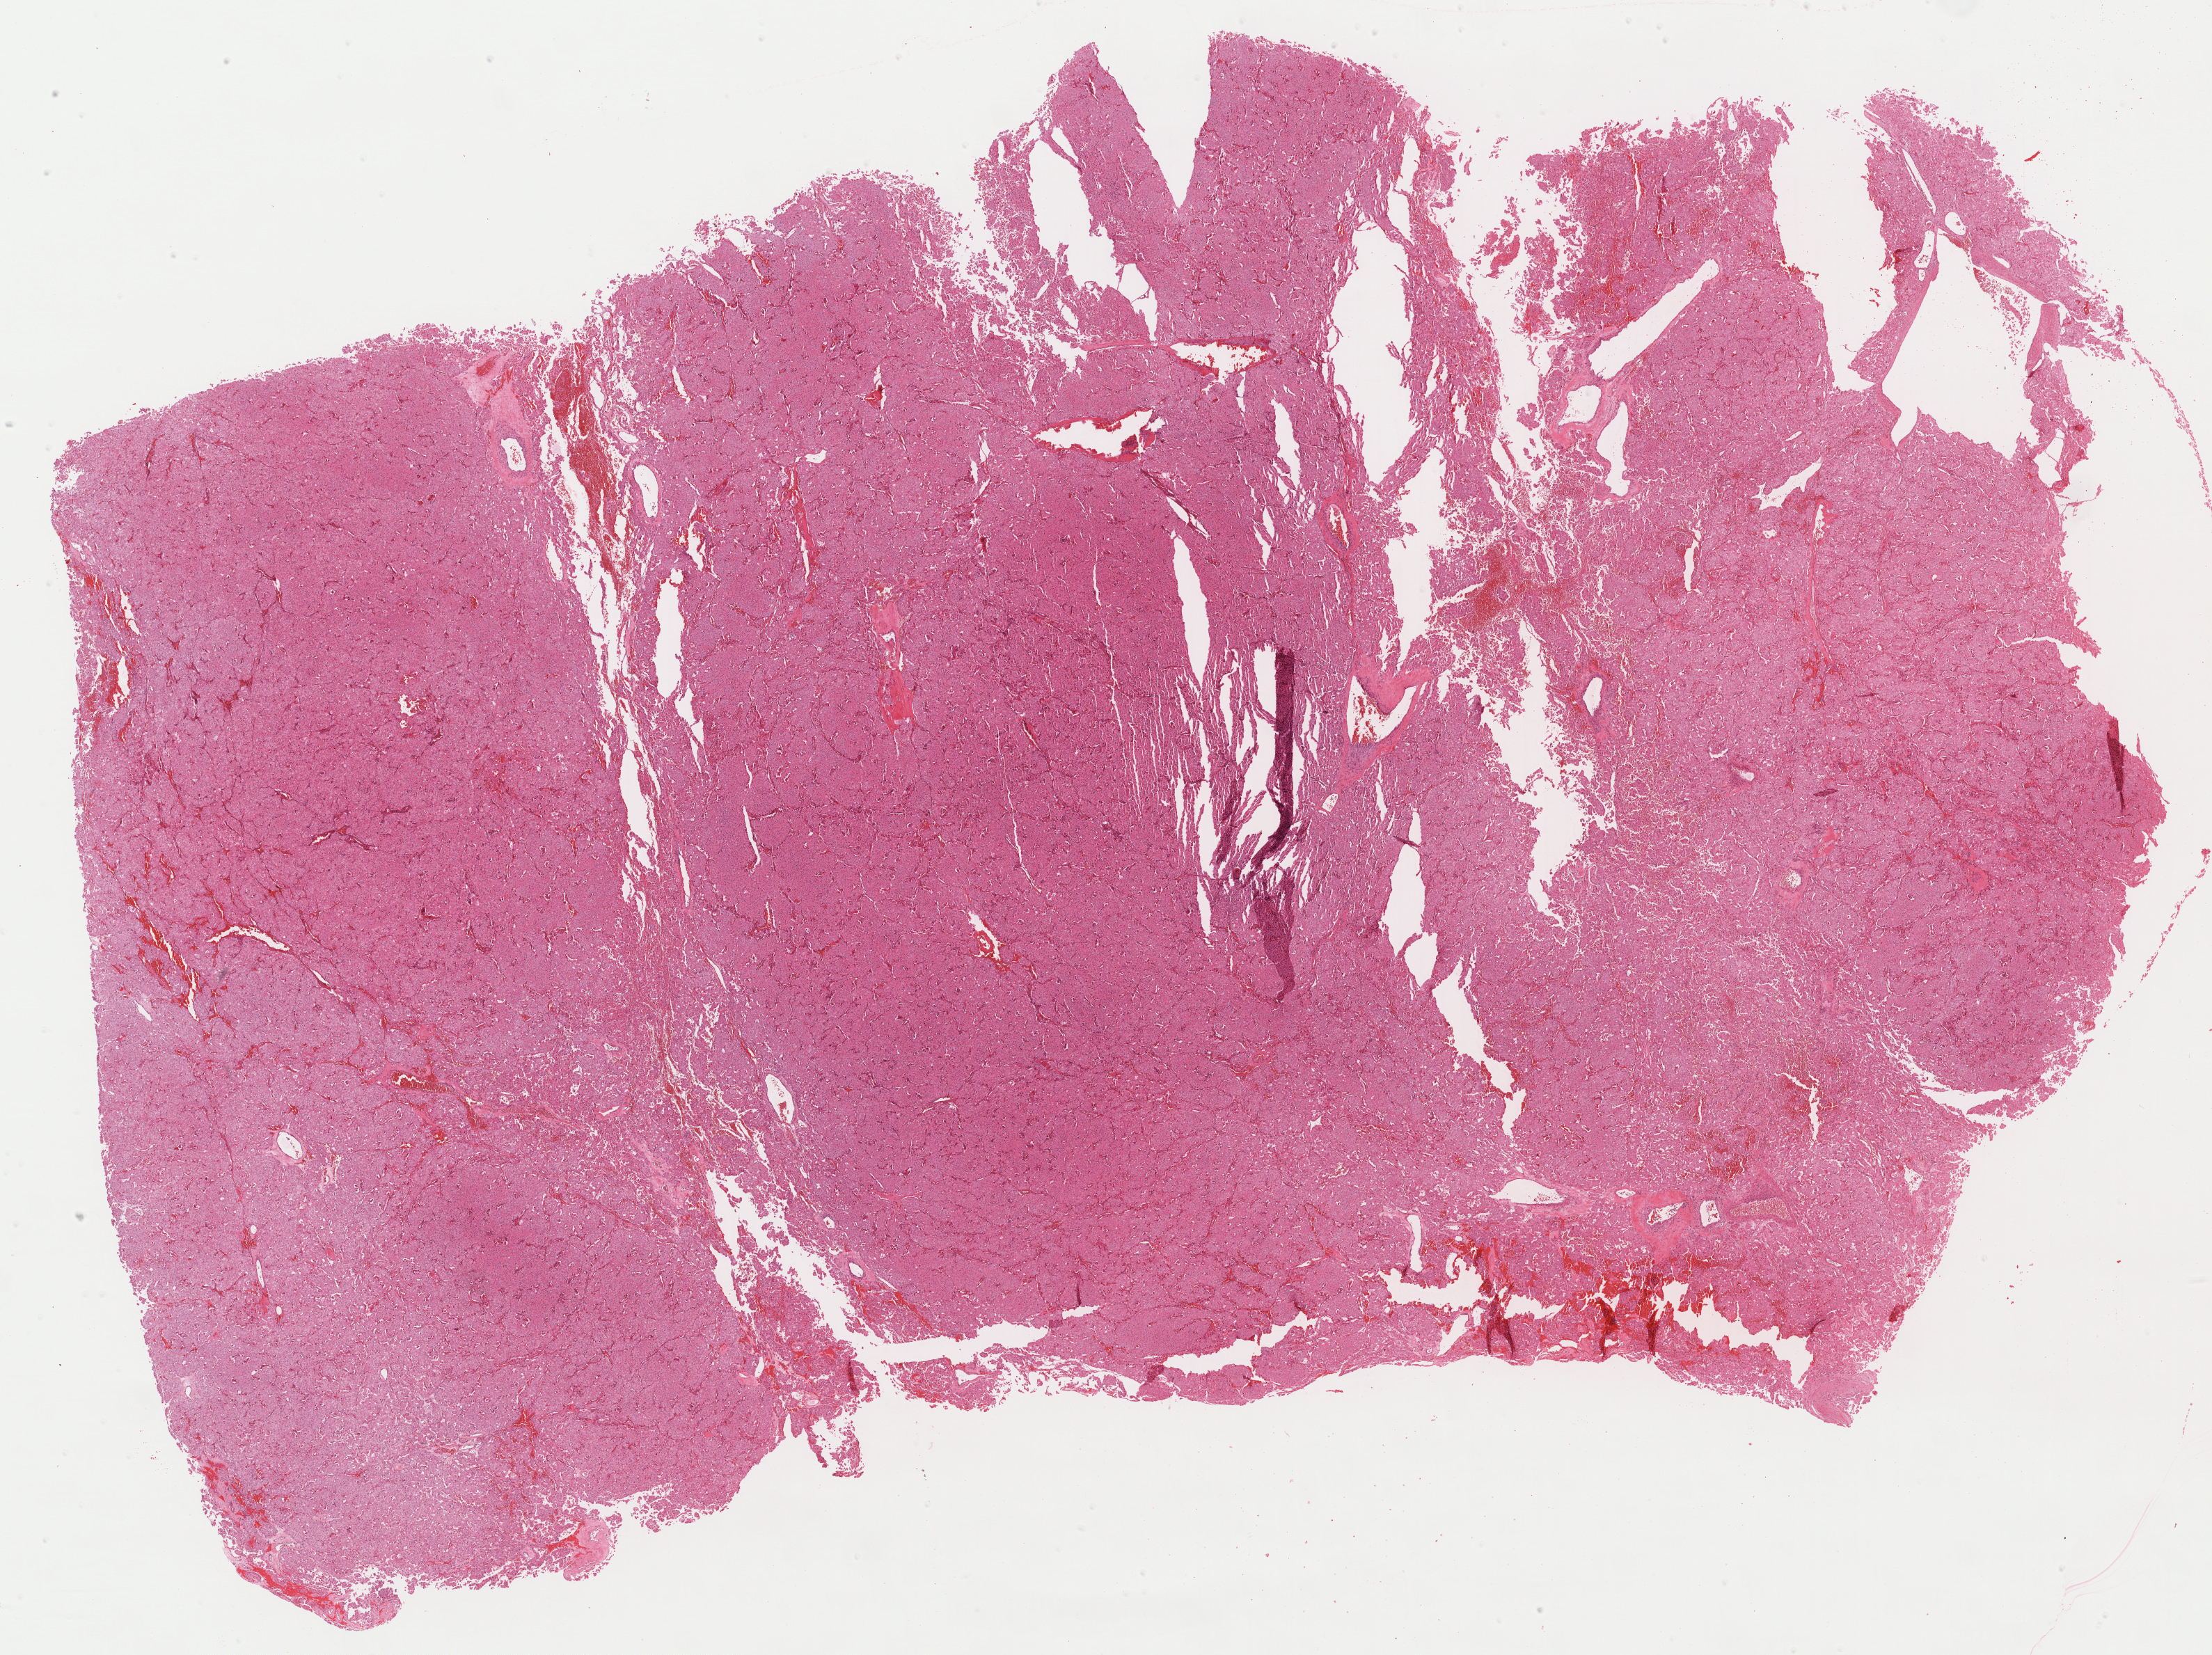
H&E whole-slide image — whole scanned area (about 25.6 x 19.2 mm) shown as a low-resolution overview, formalin-fixed paraffin-embedded (FFPE) diagnostic section, kidney, primary tumour sample. Male patient; age at initial diagnosis 43 years.
Pathologic diagnosis: Renal cell carcinoma, chromophobe type.